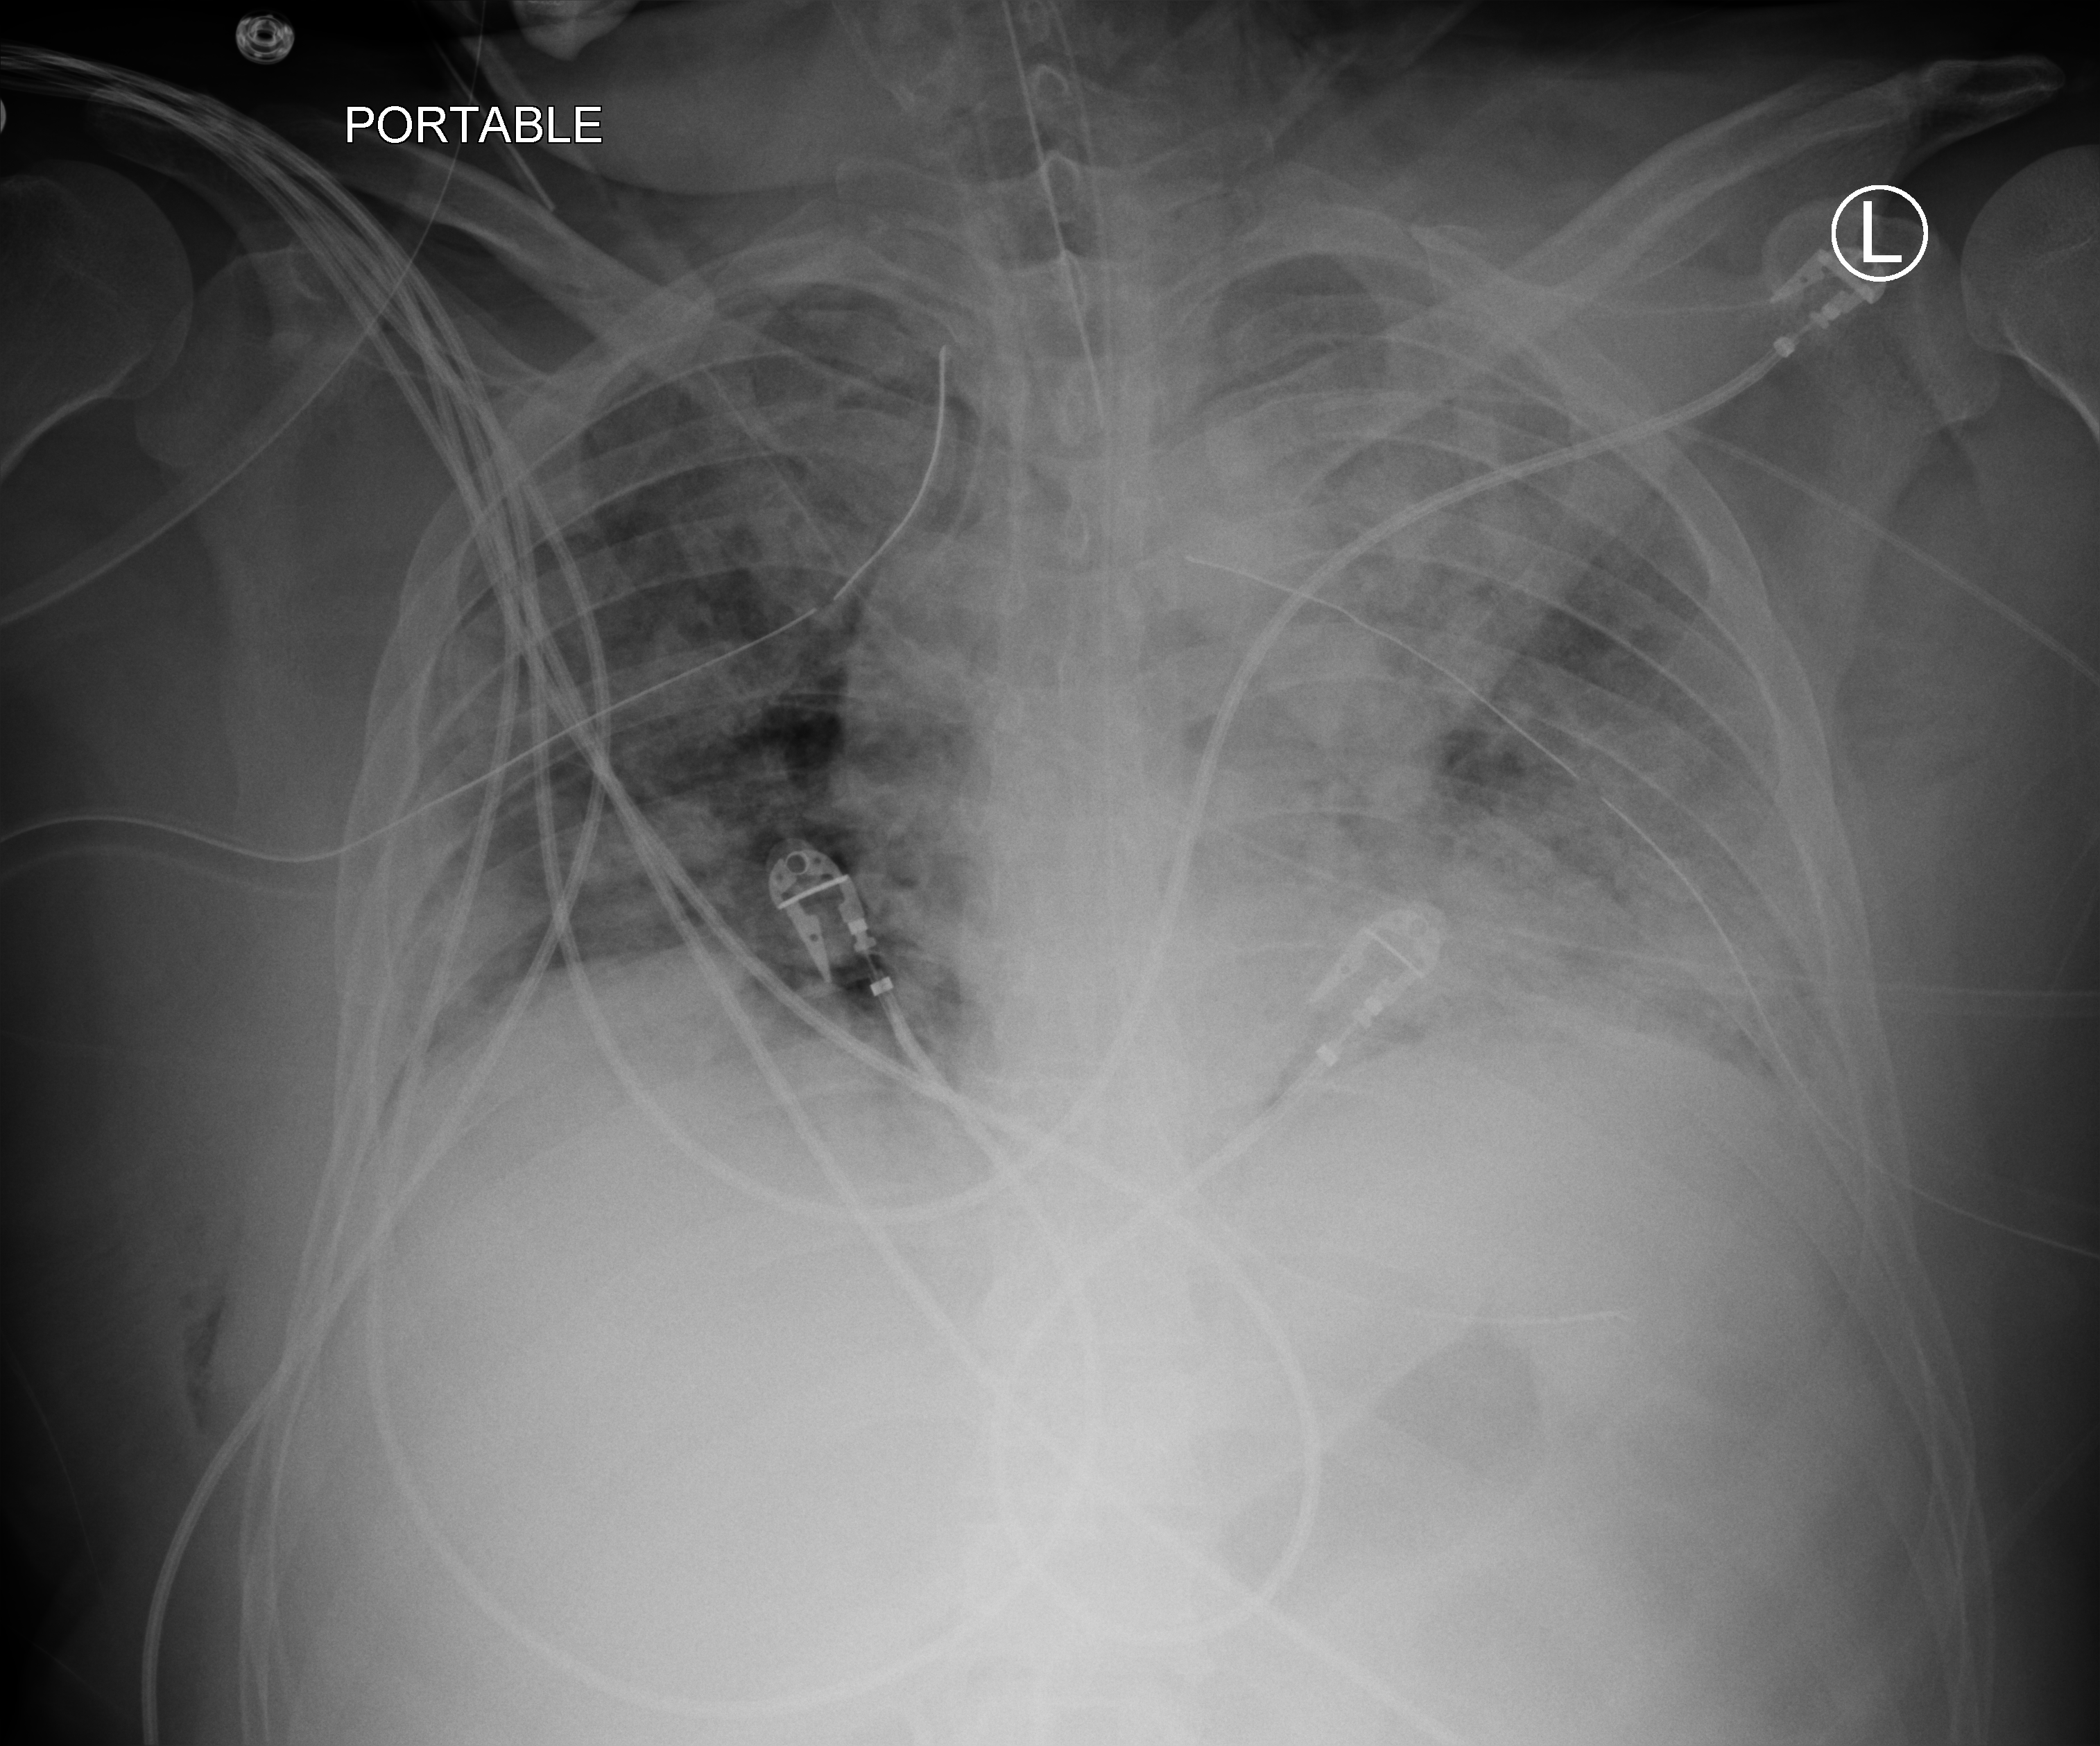
Bedside chest radiograph (computed radiography); anteroposterior (AP) projection. Male patient hospitalised with COVID-19, age 18–59 years.
Admission-level facts for this patient (not findings on this image; timing relative to this image not recorded):
- diabetes (admission record): yes
- admitted to intensive care during this hospital stay: yes
- mechanically ventilated during this hospital stay: yes